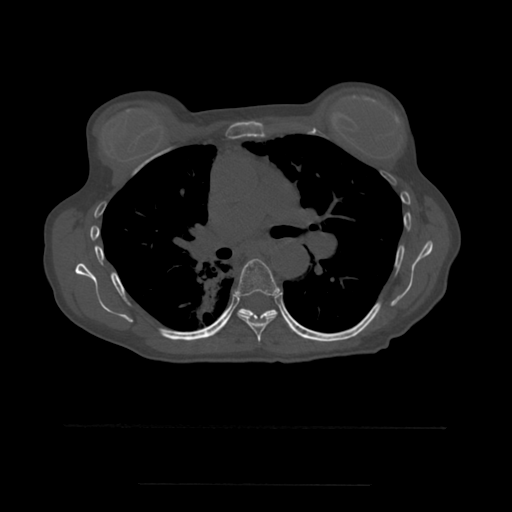
CT including the spine, one axial slice; position 370 of 544 along the scan axis; bone window (W 1800 / L 400 HU); 1.25 mm slice thickness; 512 × 512 image matrix, field of view 350 × 350 mm. Patient age 58 years. Case-level facts recorded for this patient, not image findings: primary cancer: lung.
Annotated regions visible in this slice (semi-automatically segmented with operator editing):
- T6 vertebra: bounding box (x1, y1, x2, y2) in pixels: (234, 259, 280, 343)
- T7 vertebra: (240, 309, 289, 325)